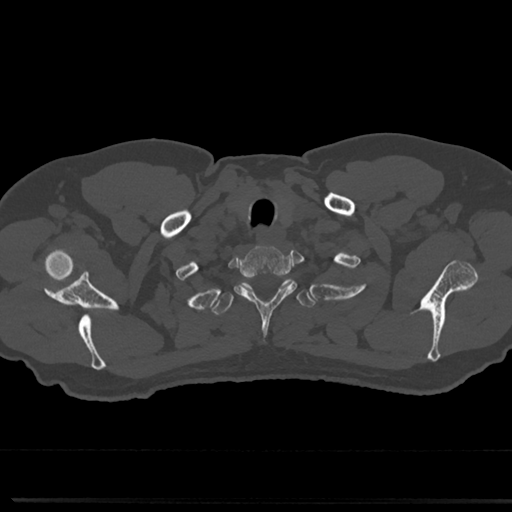
CT including the spine, one axial slice; position 661 of 817 along the scan axis; reconstruction kernel Br40s/3; 120 kVp; bone window (W 1800 / L 400 HU); 0.5 mm slice thickness; 512 × 512 image matrix, field of view 355 × 355 mm. Male patient, age 61 years. Case-level facts recorded for this patient, not image findings: primary cancer: prostate.
Annotated regions visible in this slice (semi-automatically segmented with operator editing):
- T1 vertebra: bounding box <236,247,296,303> (left, top, right, bottom; pixels)
- T2 vertebra: <214,279,314,315>